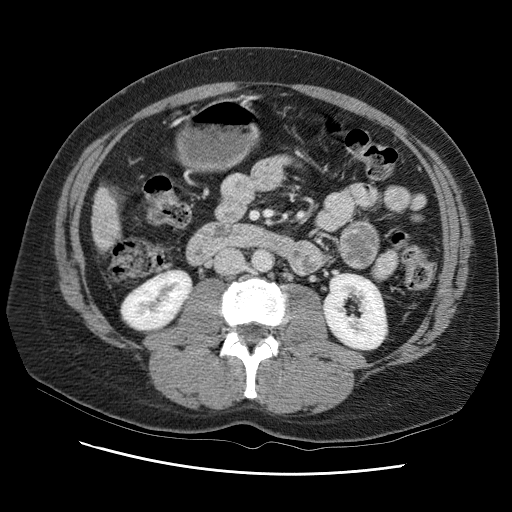
Contrast-enhanced abdominal CT (liver protocol), one axial slice; position 21 of 95 along the scan axis; reconstruction kernel STANDARD; one of 2 acquisitions stored at this slice position; soft-tissue window (W 400 / L 40 HU); 2.5 mm slice thickness; 512 × 512 image matrix, field of view 360 × 360 mm. From the clinical record (not read from this slice): diagnosis: hepatocellular carcinoma (patient treated with transarterial chemoembolisation; whether this scan precedes or follows treatment is not stated here); TNM stage (as recorded): Stage-I; Child-Pugh class: B; tumour differentiation: moderately differentiated.
Structures marked on this image (semi-automatically segmented with operator editing):
- liver parenchyma outside the tumour (the mass and vessels are separate outlines, so this box may not span the whole liver): bounding box <92,164,138,256> (left, top, right, bottom; pixels)
- liver vessels: <117,190,121,226>